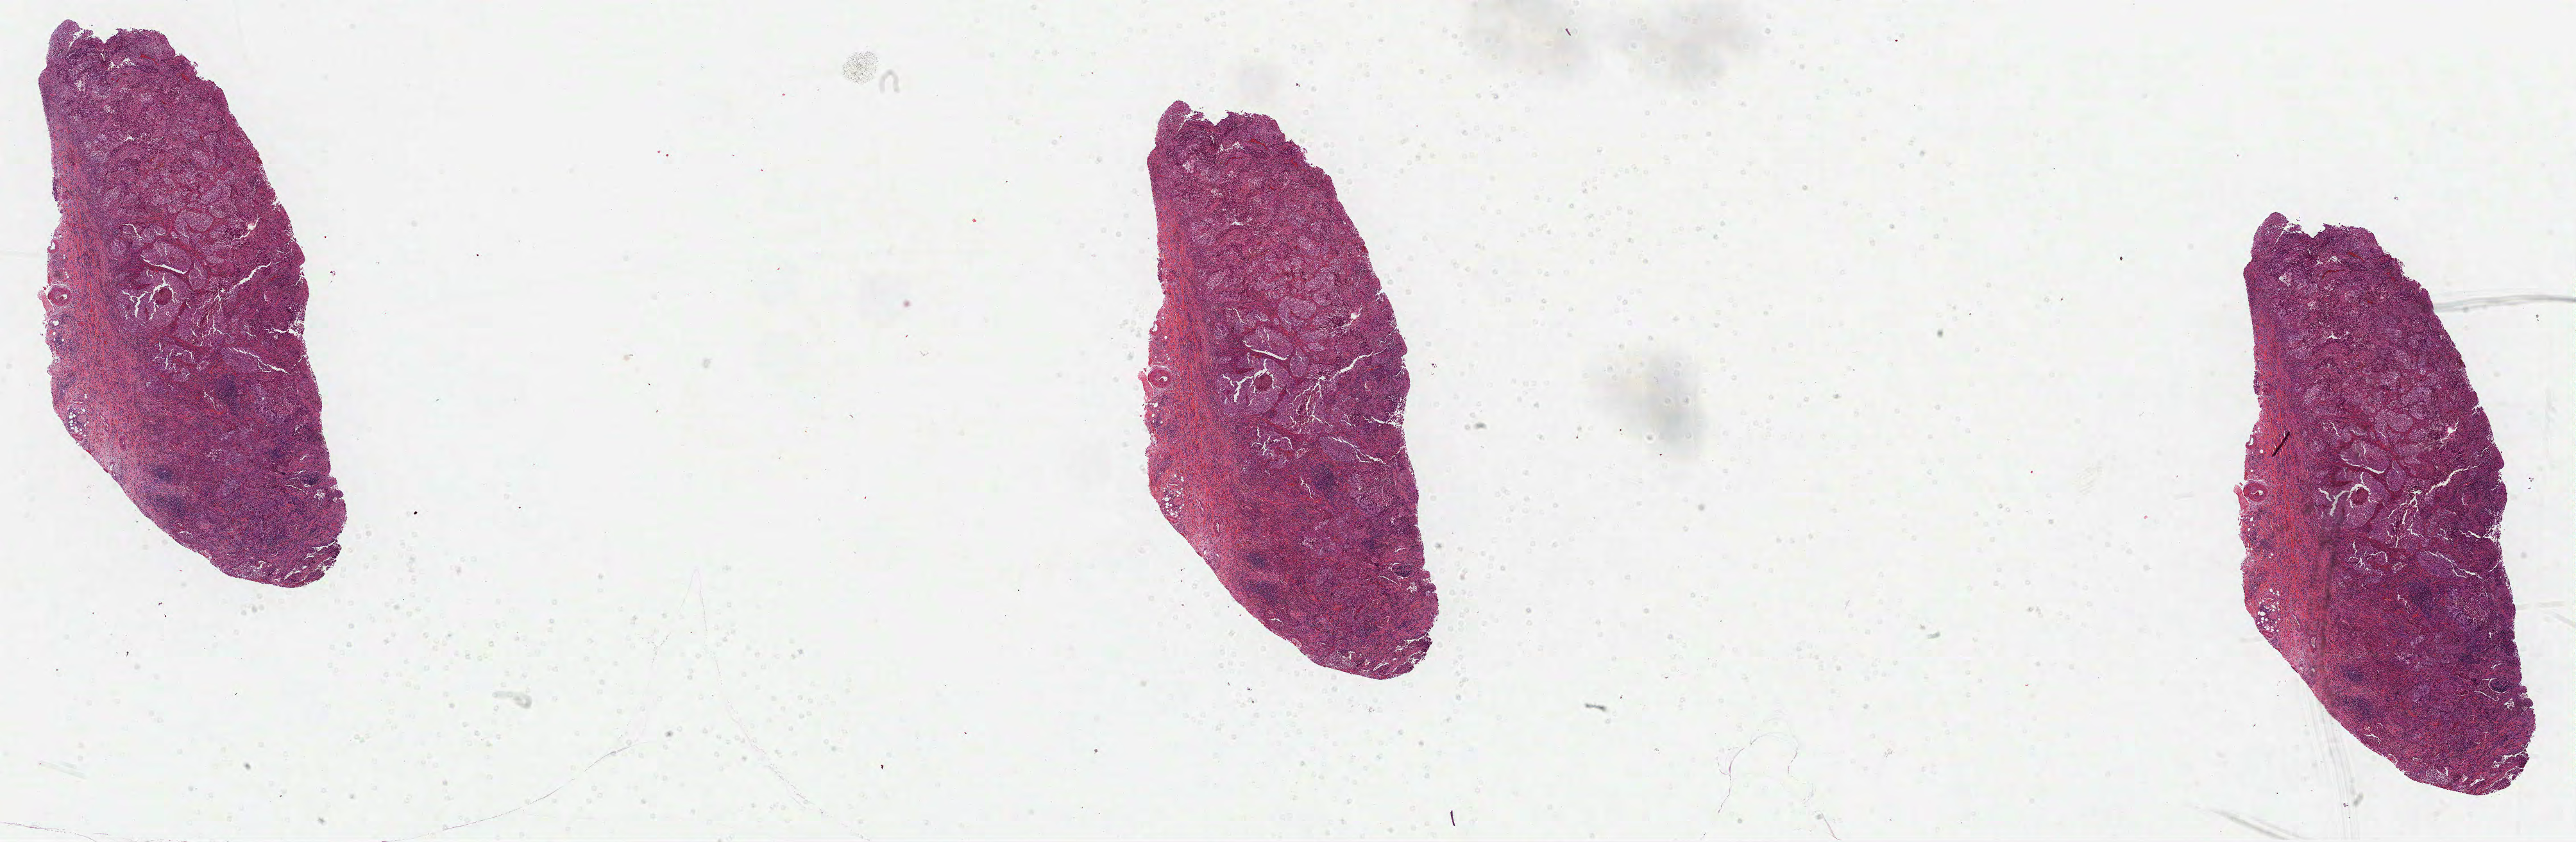
H&E-stained whole-slide image, a low-resolution overview of the entire scanned area, about 32.4 x 10.6 mm (slide scanned at 40x), formalin-fixed paraffin-embedded (FFPE) diagnostic section, lung, primary tumour sample. Male patient; age at initial diagnosis 51 years.
• AJCC pathologic stage: IB
• pathologic diagnosis: Adenocarcinoma, NOS (upper lobe, lung)
• laterality: right